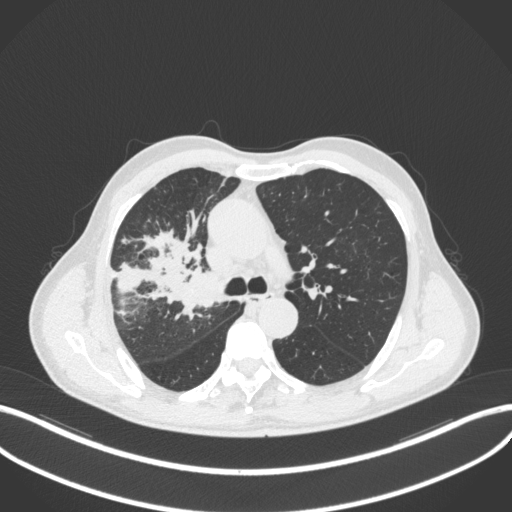
Chest CT, one axial slice; position 324 of 490 along the scan axis; reconstruction kernel B31f; 120 kVp; lung window (W 1500 / L -600 HU); 1 mm slice thickness; 512 × 512 image matrix, field of view 400 × 400 mm. Male patient, age 69 years. From the clinical record (not read from this slice): clinical TNM (as recorded): T2a N0 M0.
Annotated regions visible in this slice (bounding box drawn by a radiologist):
- lung tumour (recorded histology: adenocarcinoma): box from (x=180, y=271) to (x=220, y=313) px